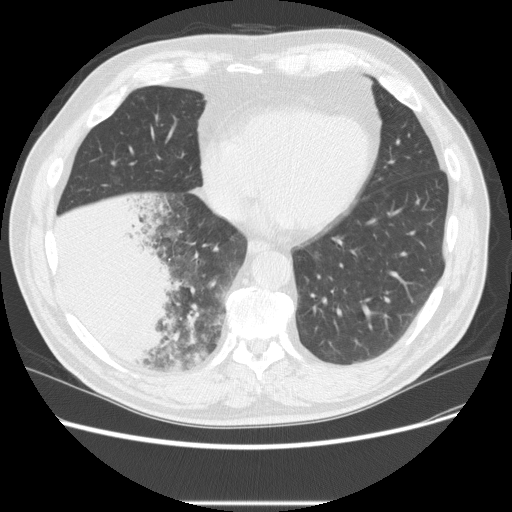
Low-dose screening chest CT, one axial slice. Slice 74 of 233 in the series (ordered by position). Reconstruction kernel STANDARD. 120 kVp. Lung window (W 1500 / L -600 HU). 512 × 512 image matrix, field of view 380 × 380 mm.
Annotated regions visible in this slice (expert manual segmentation):
- lesion 3 (tumor, lower lobe of right lung): box from (x=53, y=194) to (x=179, y=367) px